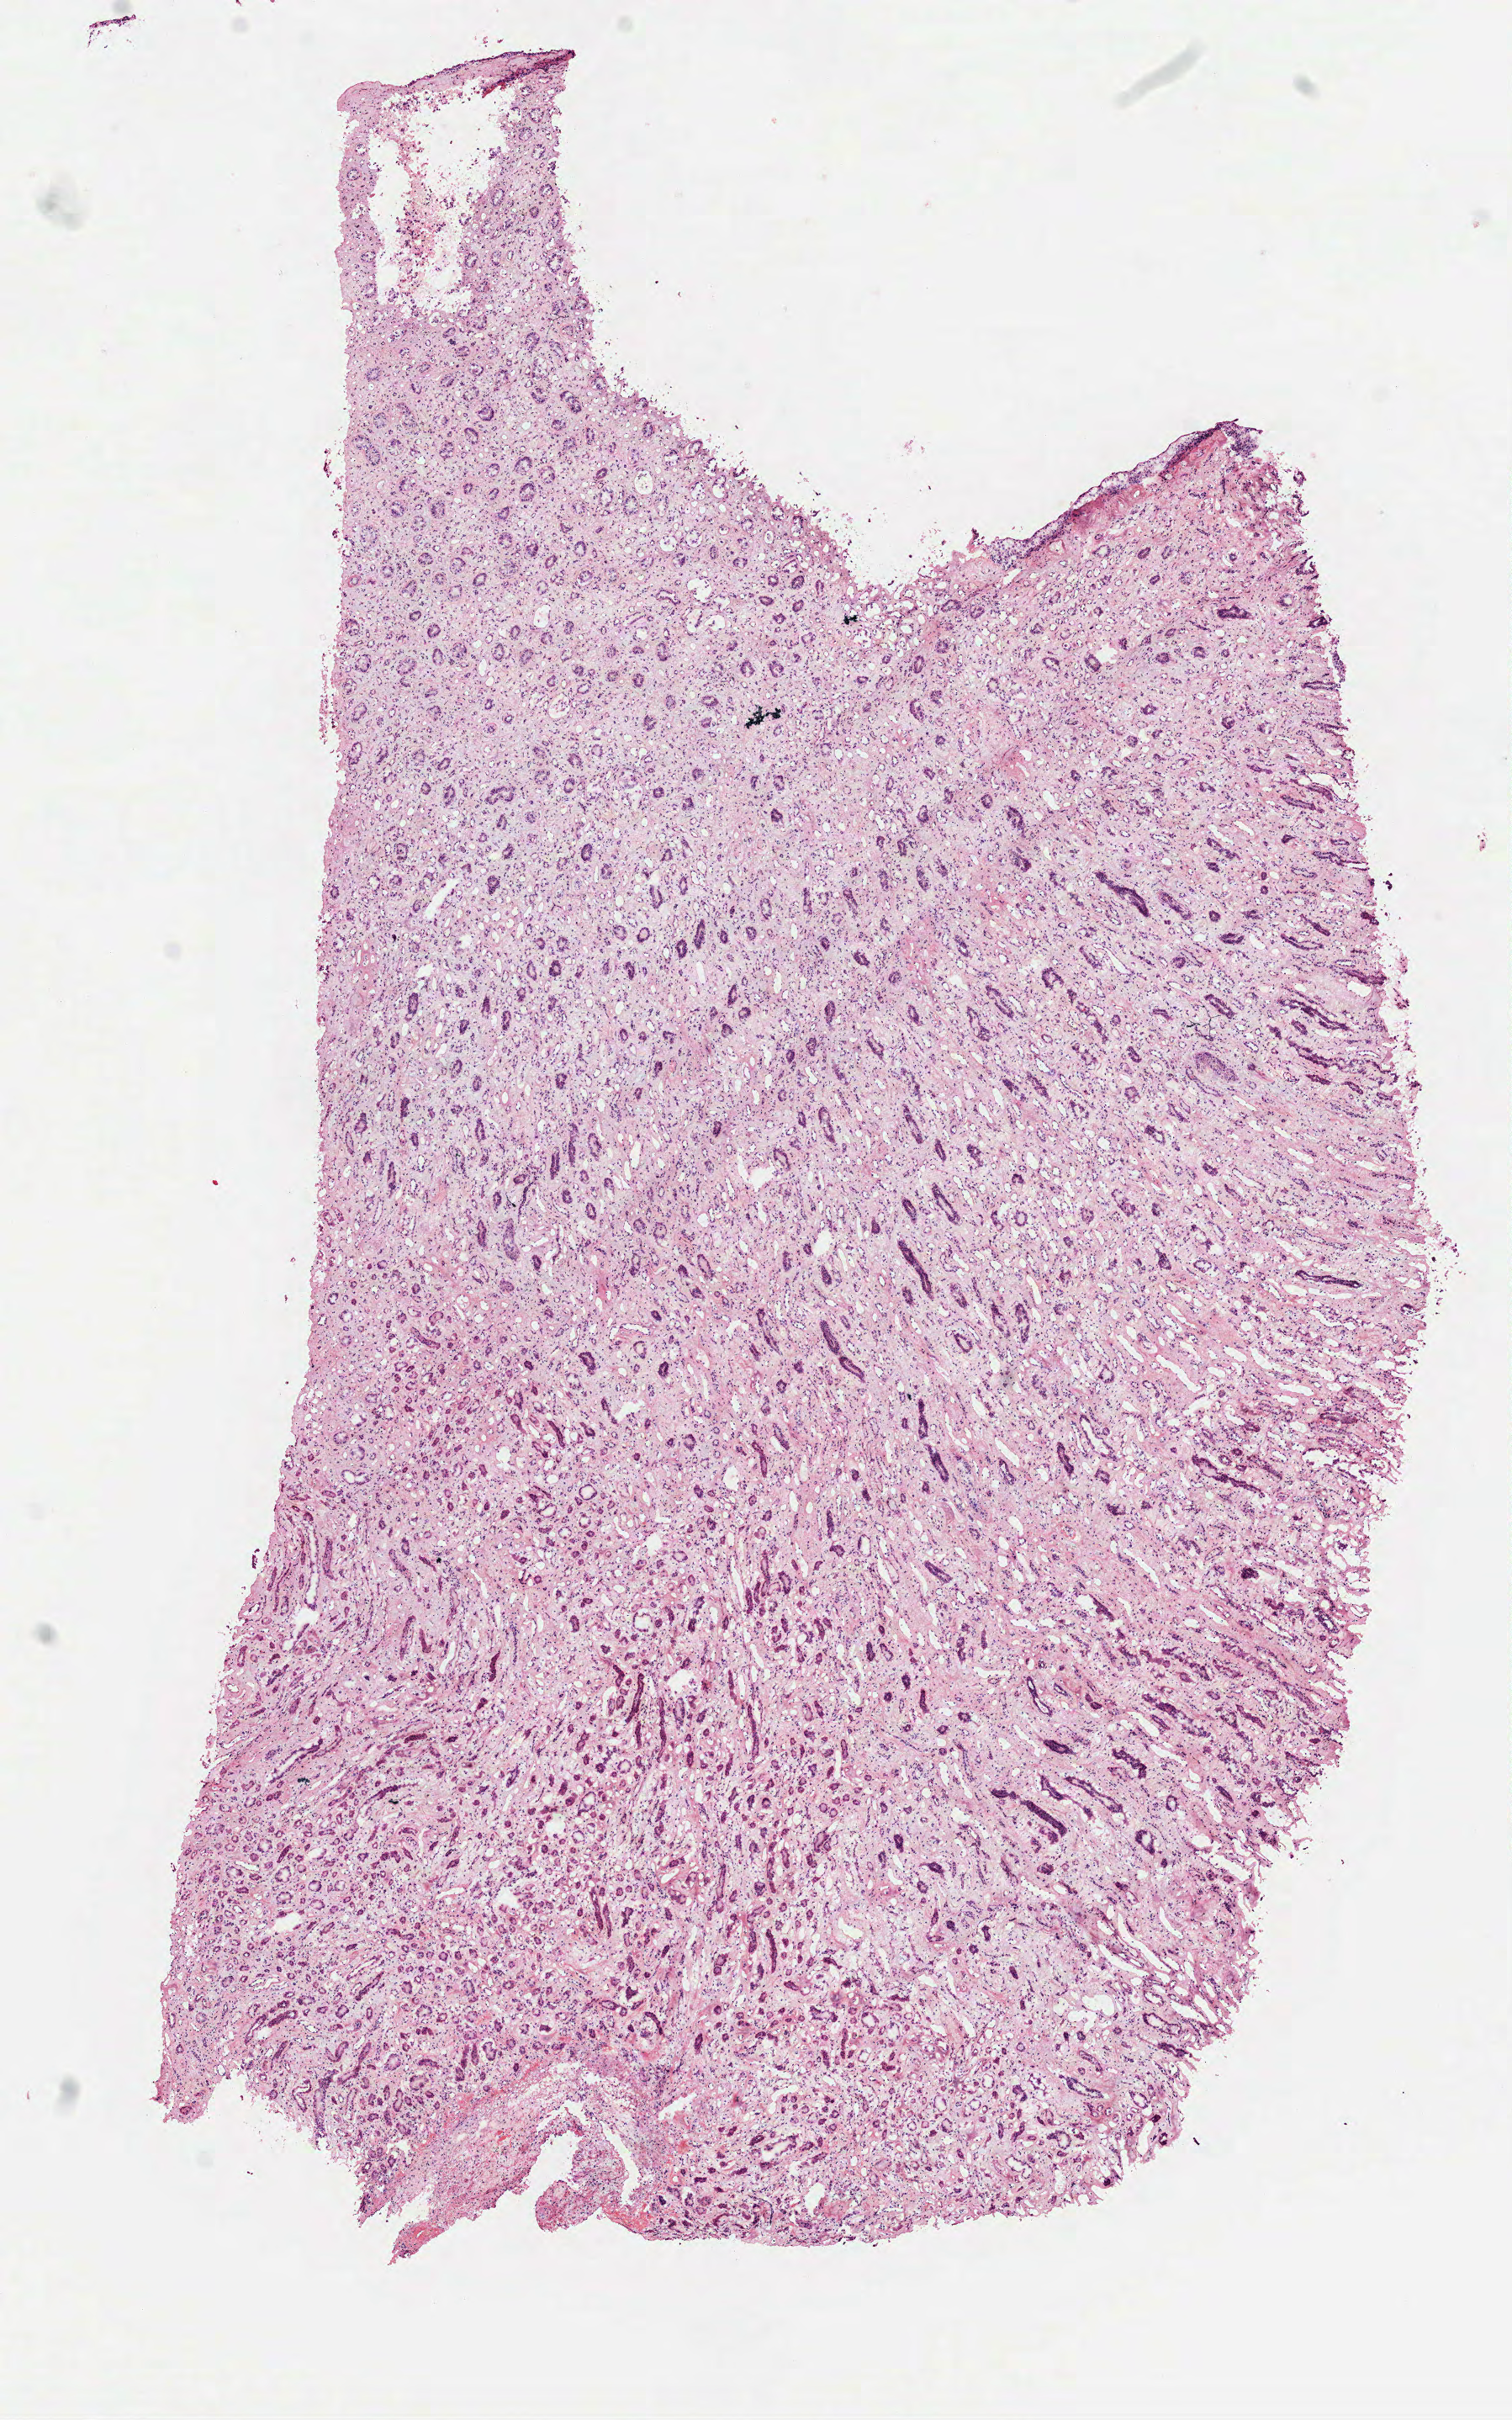
H&E-stained whole-slide image, whole scanned area (about 7.3 x 11.6 mm) shown as a low-resolution overview. Frozen section. Kidney, solid tissue normal (non-tumour tissue) sample. Patient: female, age at initial diagnosis 83 years.
This section: solid tissue normal (non-tumour) sample from the same patient. Patient diagnosis: Papillary adenocarcinoma, NOS.